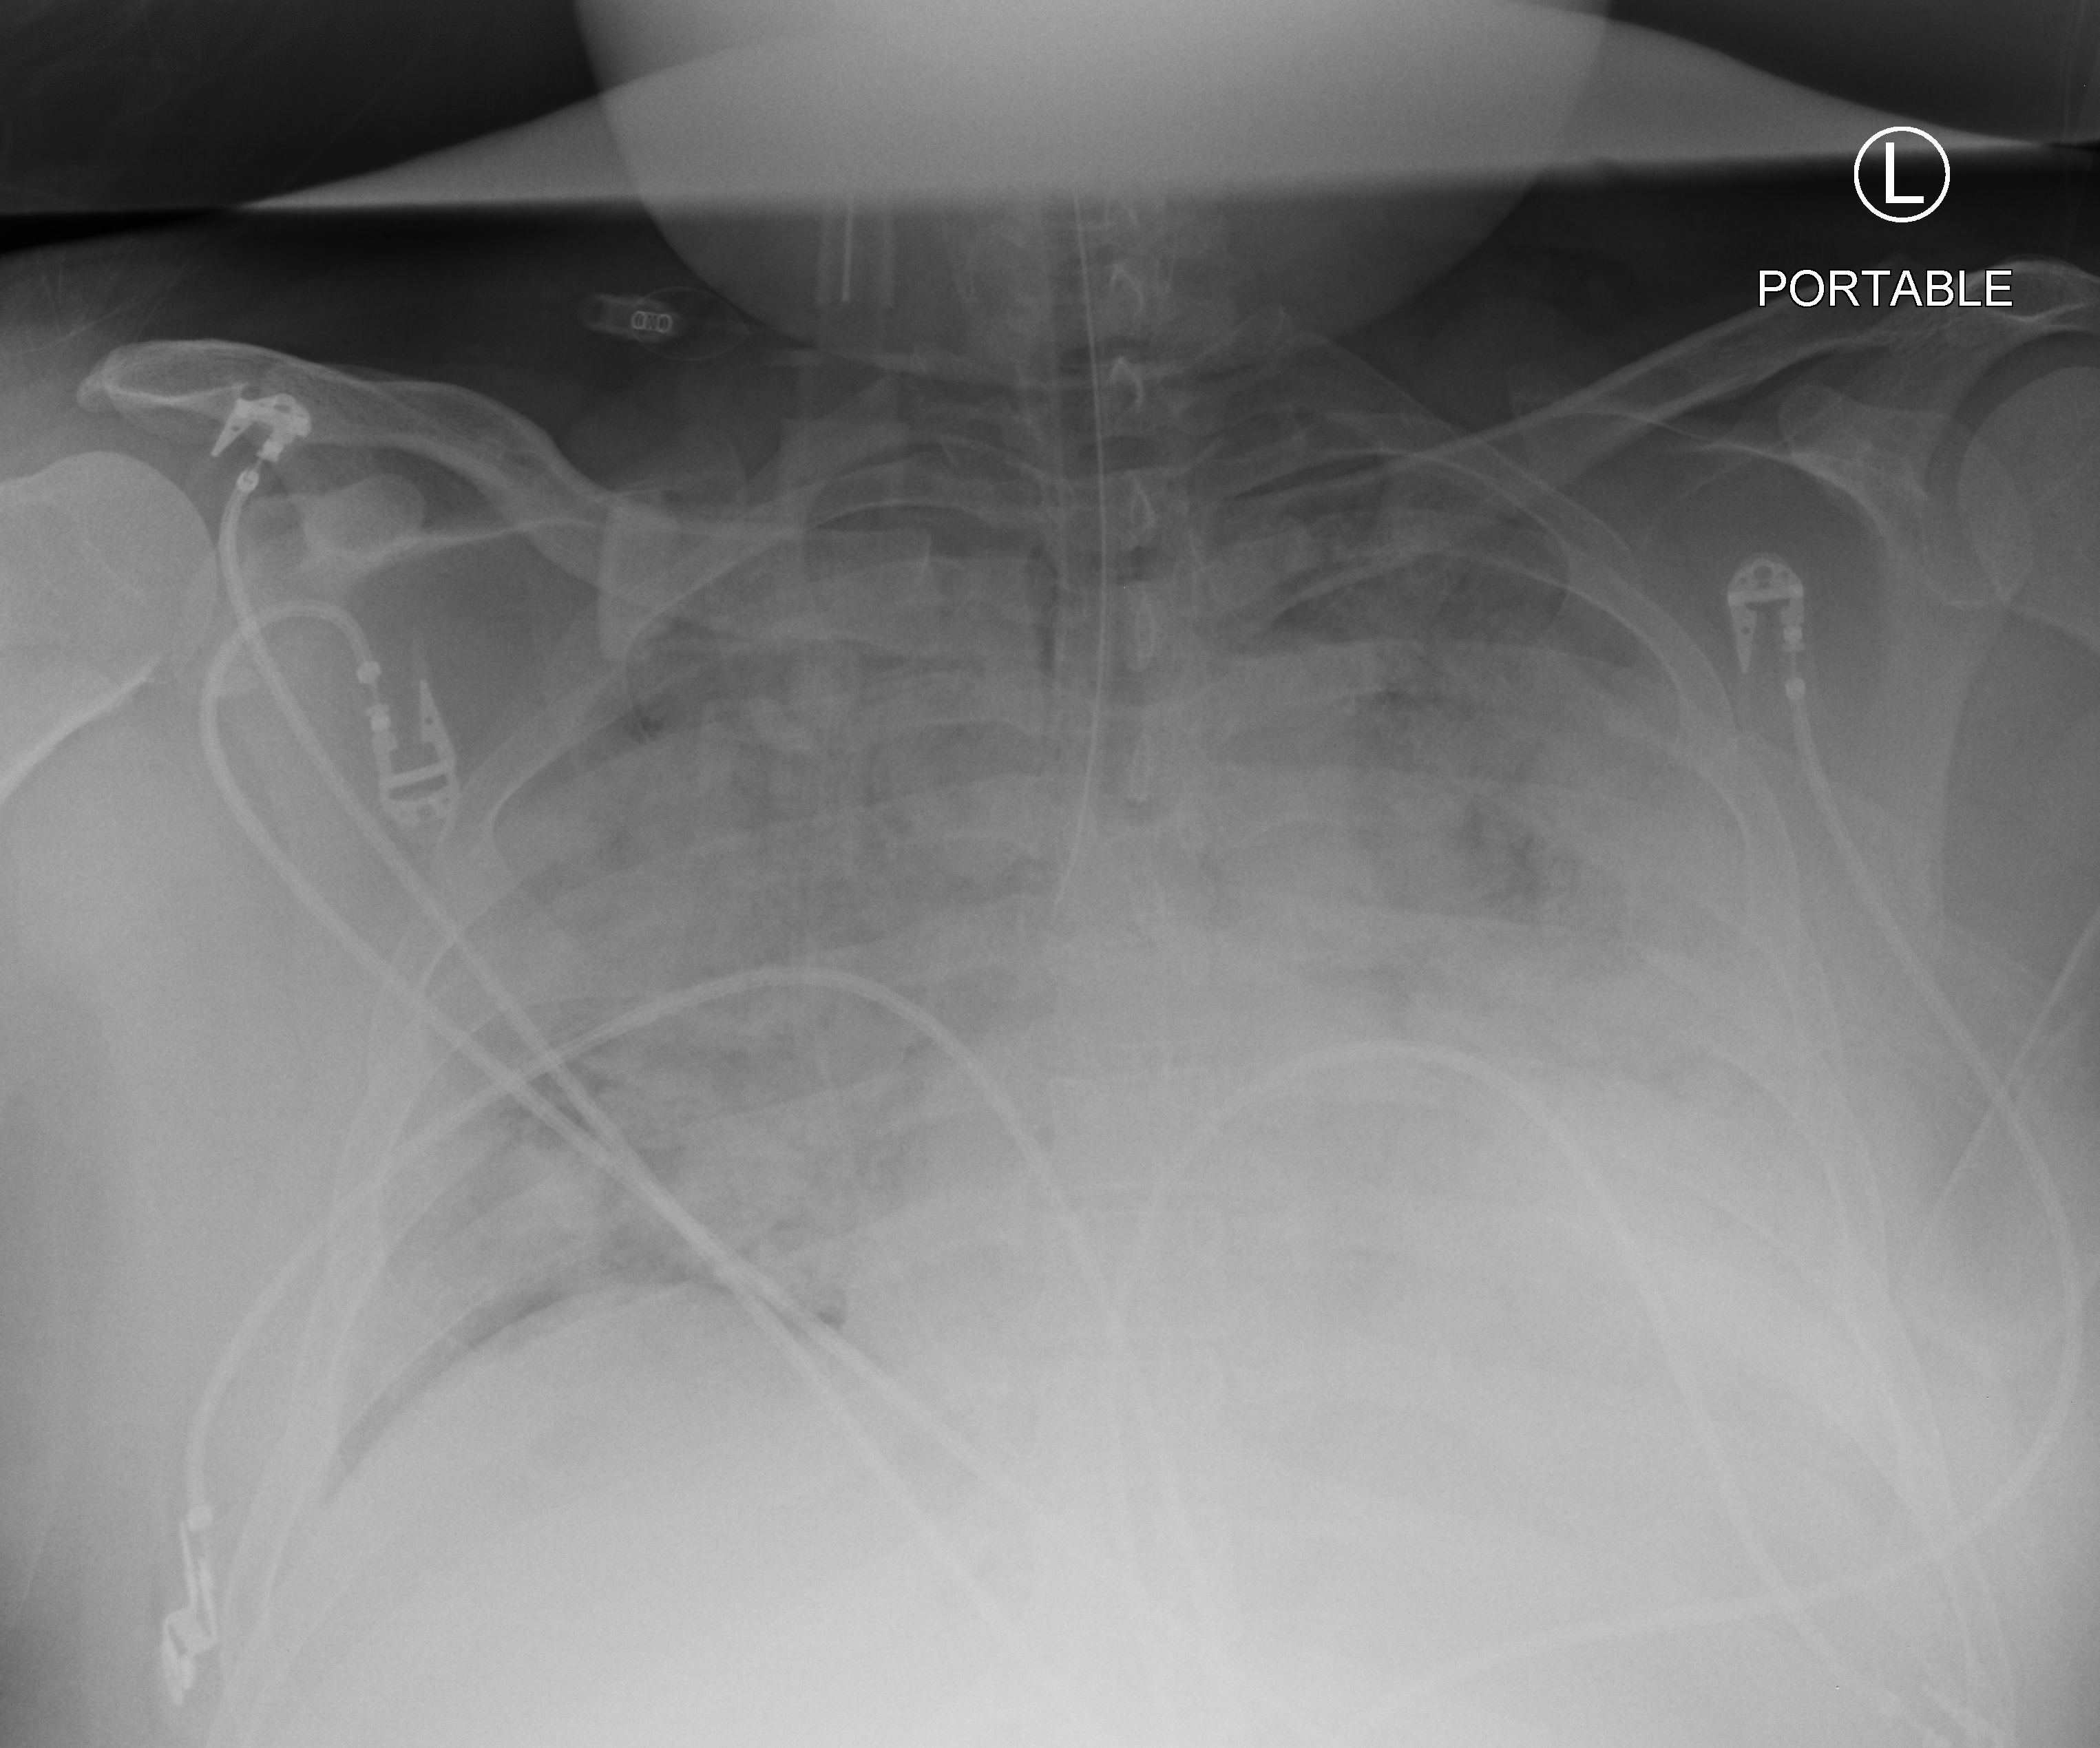
Portable chest radiograph; anteroposterior (AP) projection. Patient hospitalised with COVID-19, aged 18–59 years.
Hospital-stay facts (about this admission, not read from this image; timing relative to this image not recorded): mechanically ventilated during this hospital stay: yes; admitted to intensive care during this hospital stay: yes; hypertension (admission record): no.